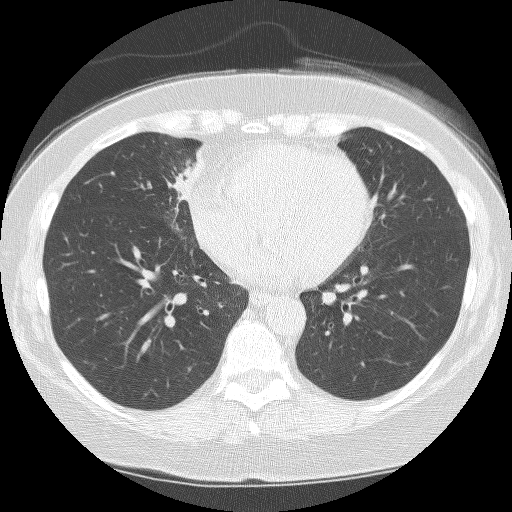
Low-dose screening chest CT, one axial slice. Slice 74 of 159 in the series (ordered by position). 120 kVp. Lung window (W 1500 / L -600 HU). 2.5 mm slice thickness. 512 × 512 image matrix, field of view 299 × 299 mm.
Structures marked on this image (outlined manually by an expert reader):
- lesion 1 (tumor, hilum of right lung): box from (x=166, y=145) to (x=204, y=201) px